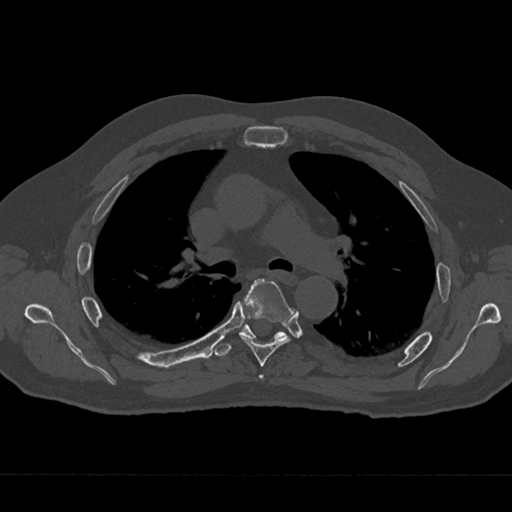
CT including the spine, one axial slice. Position 456 of 797 along the scan axis. 120 kVp. Bone window (W 1800 / L 400 HU). 512 × 512 image matrix, field of view 377 × 377 mm. Patient: male, 75 years. Case-level facts recorded for this patient, not image findings: primary cancer: renal; vertebrae with lytic lesions (as recorded): T4.
Outlined on this slice (semi-automatically segmented with operator editing):
- T4 vertebra: box from (x=259, y=374) to (x=264, y=380) px
- T5 vertebra: (x=239, y=278)–(x=293, y=367)
- T6 vertebra: (x=215, y=310)–(x=286, y=357)